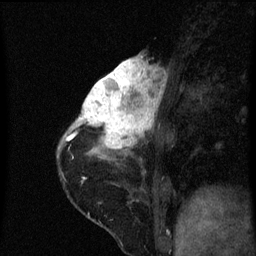
Breast MRI (dynamic contrast-enhanced), one sagittal slice. Slice 22 of 60 in the series (ordered by position). Dynamic contrast-enhanced series, image 2 of 3 at this slice position (ordered by acquisition). 1.5 T. TE 4.2 ms, TR 8 ms. 2 mm slice thickness. 256 × 256 image matrix, field of view 180 × 180 mm. Female patient, age 38 years.
Outlined on this slice (semi-automatically segmented with operator editing):
- analysis volume of interest (the breast-tissue region the enhancement analysis was run in; not a lesion): bounding box <80,58,167,151> (left, top, right, bottom; pixels)
- tumour enhancement mask (voxels above the 70 % enhancement threshold inside the analysis volume of interest): <80,58,161,149>